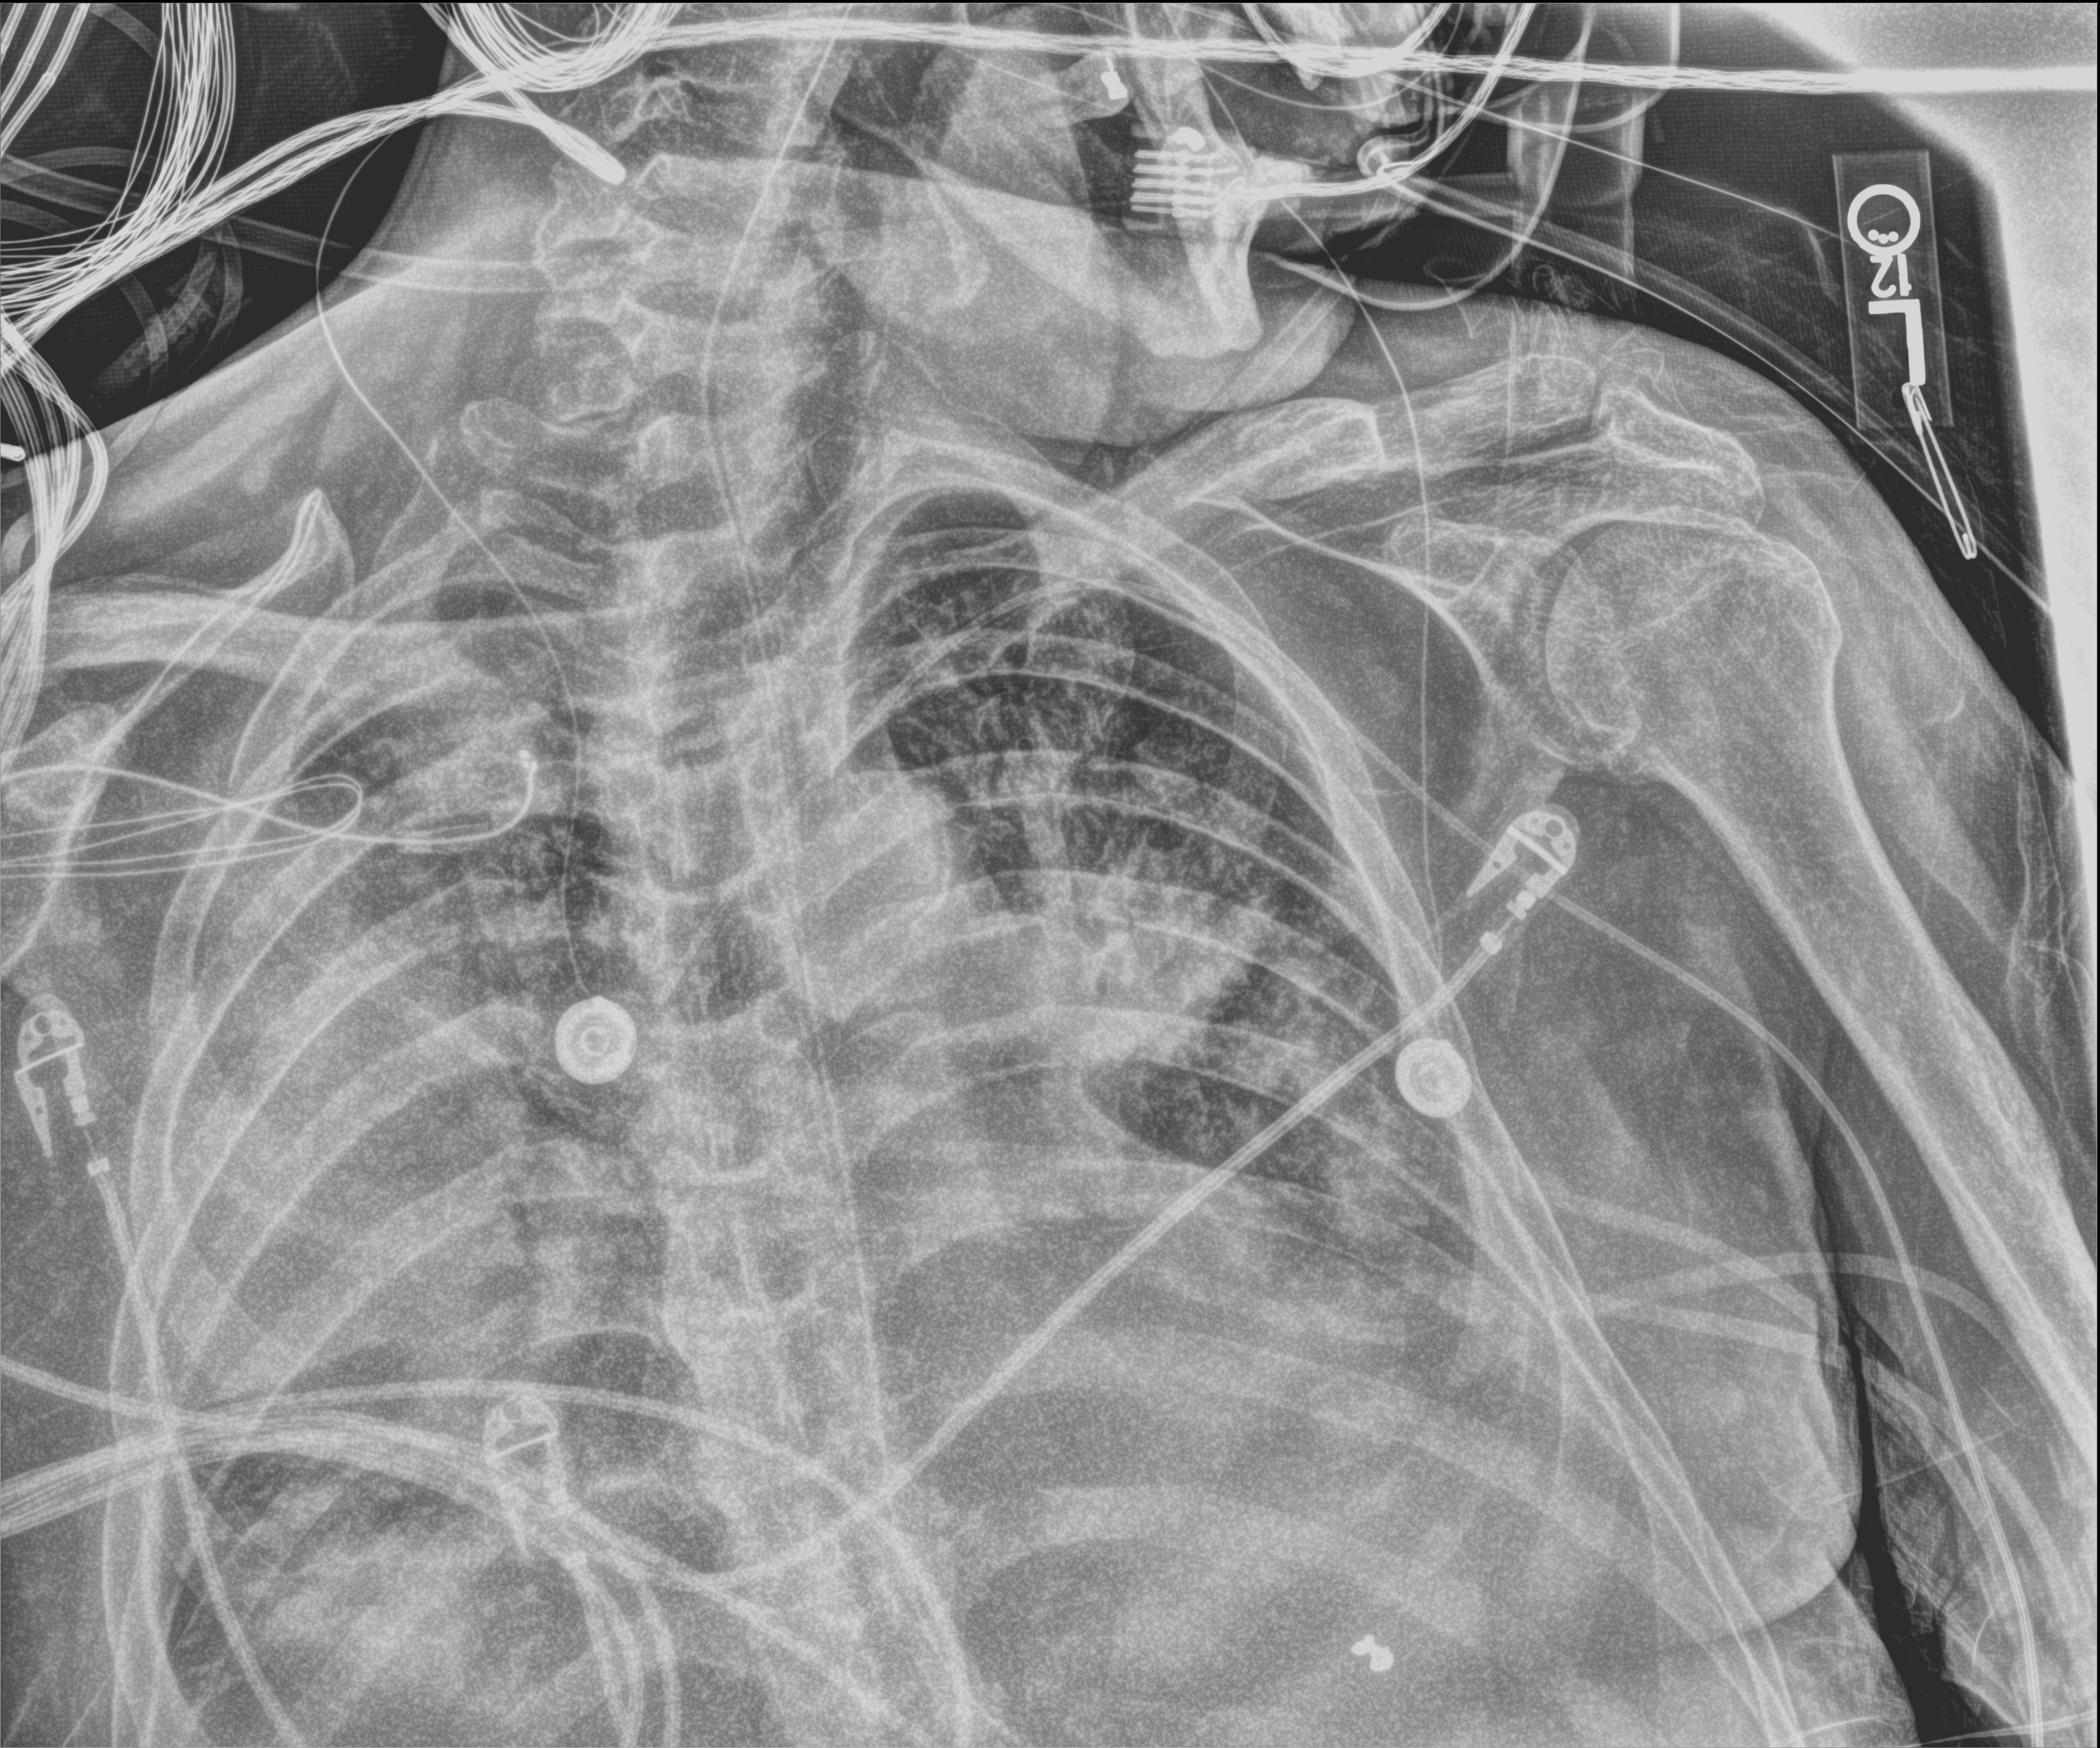
Portable chest radiograph. Male patient hospitalised with COVID-19, age 60–74 years.
From the hospital-stay record, not from the radiograph (when in the stay this image was taken is not recorded): mechanically ventilated during this hospital stay: no.